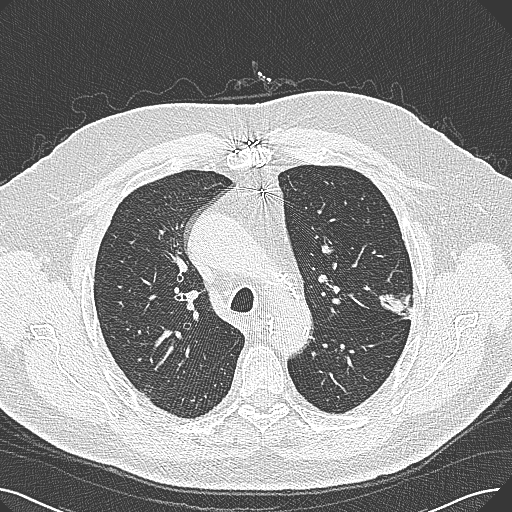
Axial slice from a low-dose chest CT screening exam. Baseline annual screen. Lung window (W 1500 / L -600 HU). 1 mm slice thickness. Lung (sharp) reconstruction kernel (B80f). Slice 87 of 269 in the series. 512 × 512 image matrix. Male, age 74 years at enrolment. Former smoker at enrolment.
Expert reader's lesion annotation, bounding box (x1, y1, x2, y2) in pixels: (369, 273, 426, 322). The exam's reader record, not a measurement of the box and not confirmed to be the same lesion: non-calcified nodule or mass ≥4 mm, left upper lobe, 15 × 10 mm, poorly defined margins, soft tissue attenuation. Official screen result: positive, change unspecified: nodule(s) >= 4 mm or enlarging nodule(s), mass(es), or other non-specific abnormalities suspicious for lung cancer. Later outcome: lung cancer diagnosed 124 days after this screen — adenocarcinoma, NOS, left upper lobe, well differentiated (G1), stage IA (AJCC 6th edition), 26 mm at pathology.